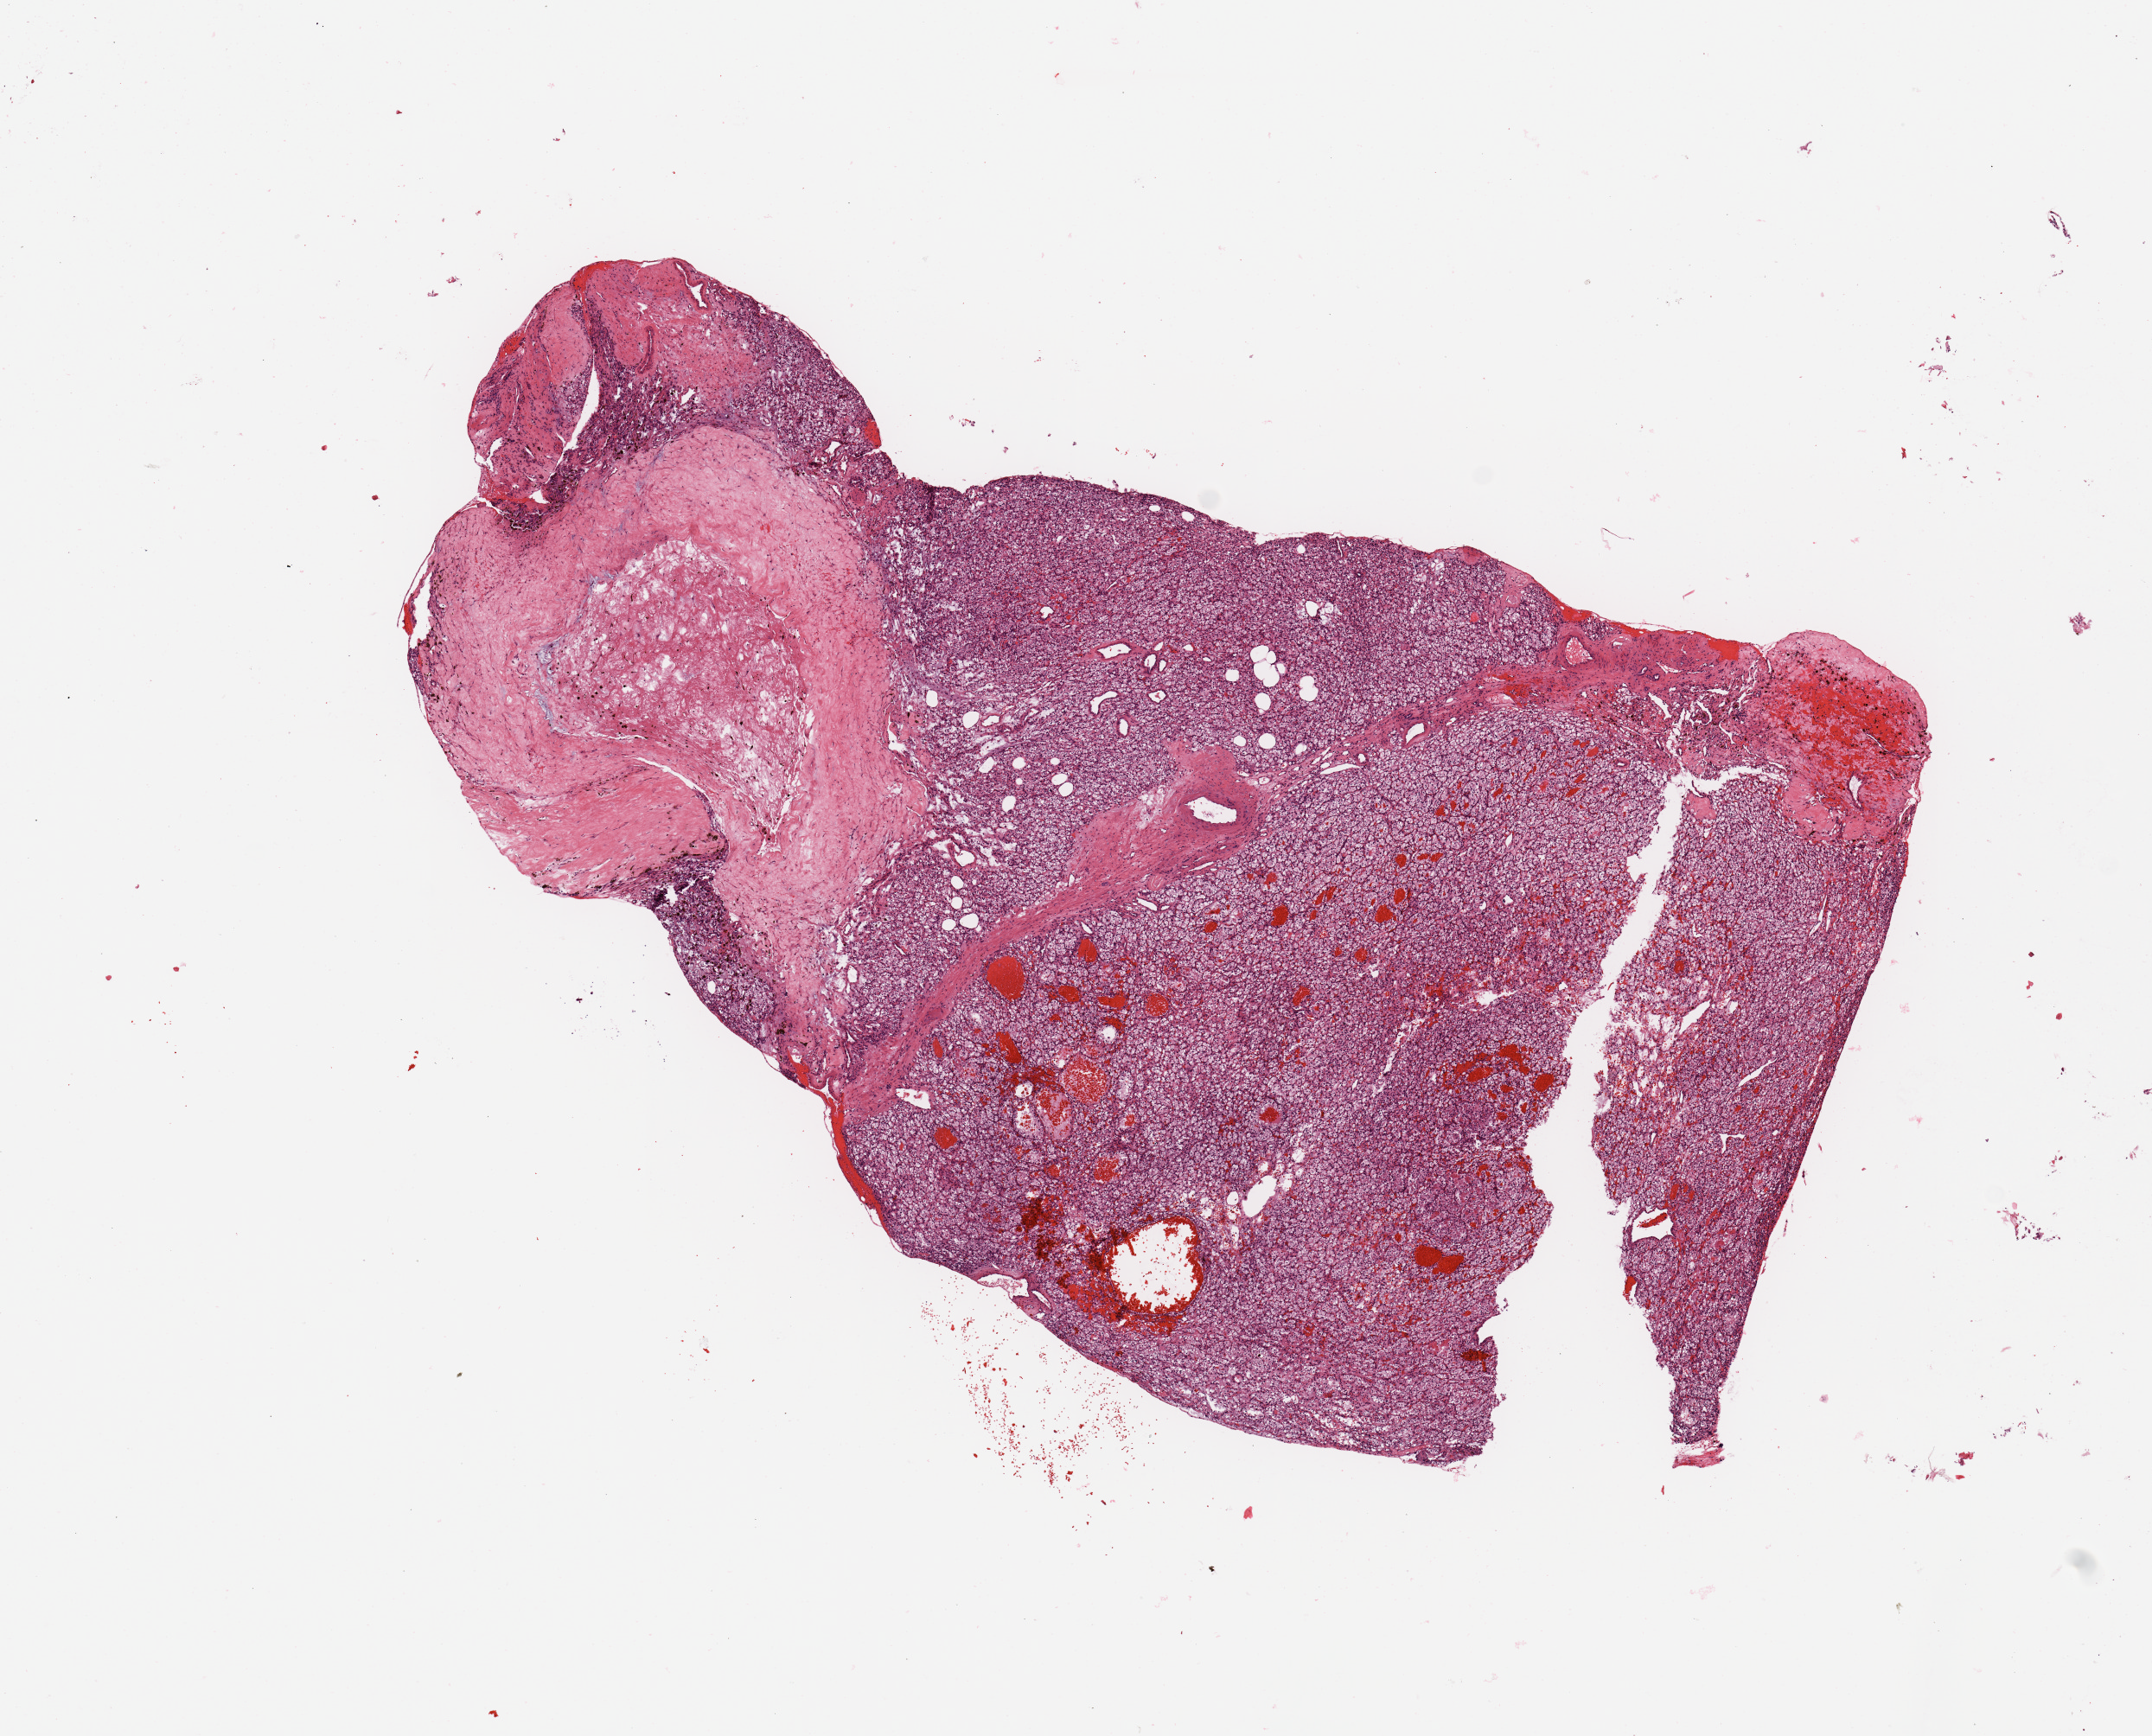
H&E-stained whole-slide image, low-resolution overview of the scanned area, about 9.8 x 7.9 mm (slide scanned at 20x). Tumour tissue sample, sampled site: kidney. 64-year-old female patient. Histologic grade: G2 (moderately differentiated). Composition of this section per pathologist review: tumour nuclei 85%, necrosis 3%.
- AJCC pathologic stage: I
- primary tumour site (as recorded): lower pole
- diagnosis: Renal cell carcinoma, NOS